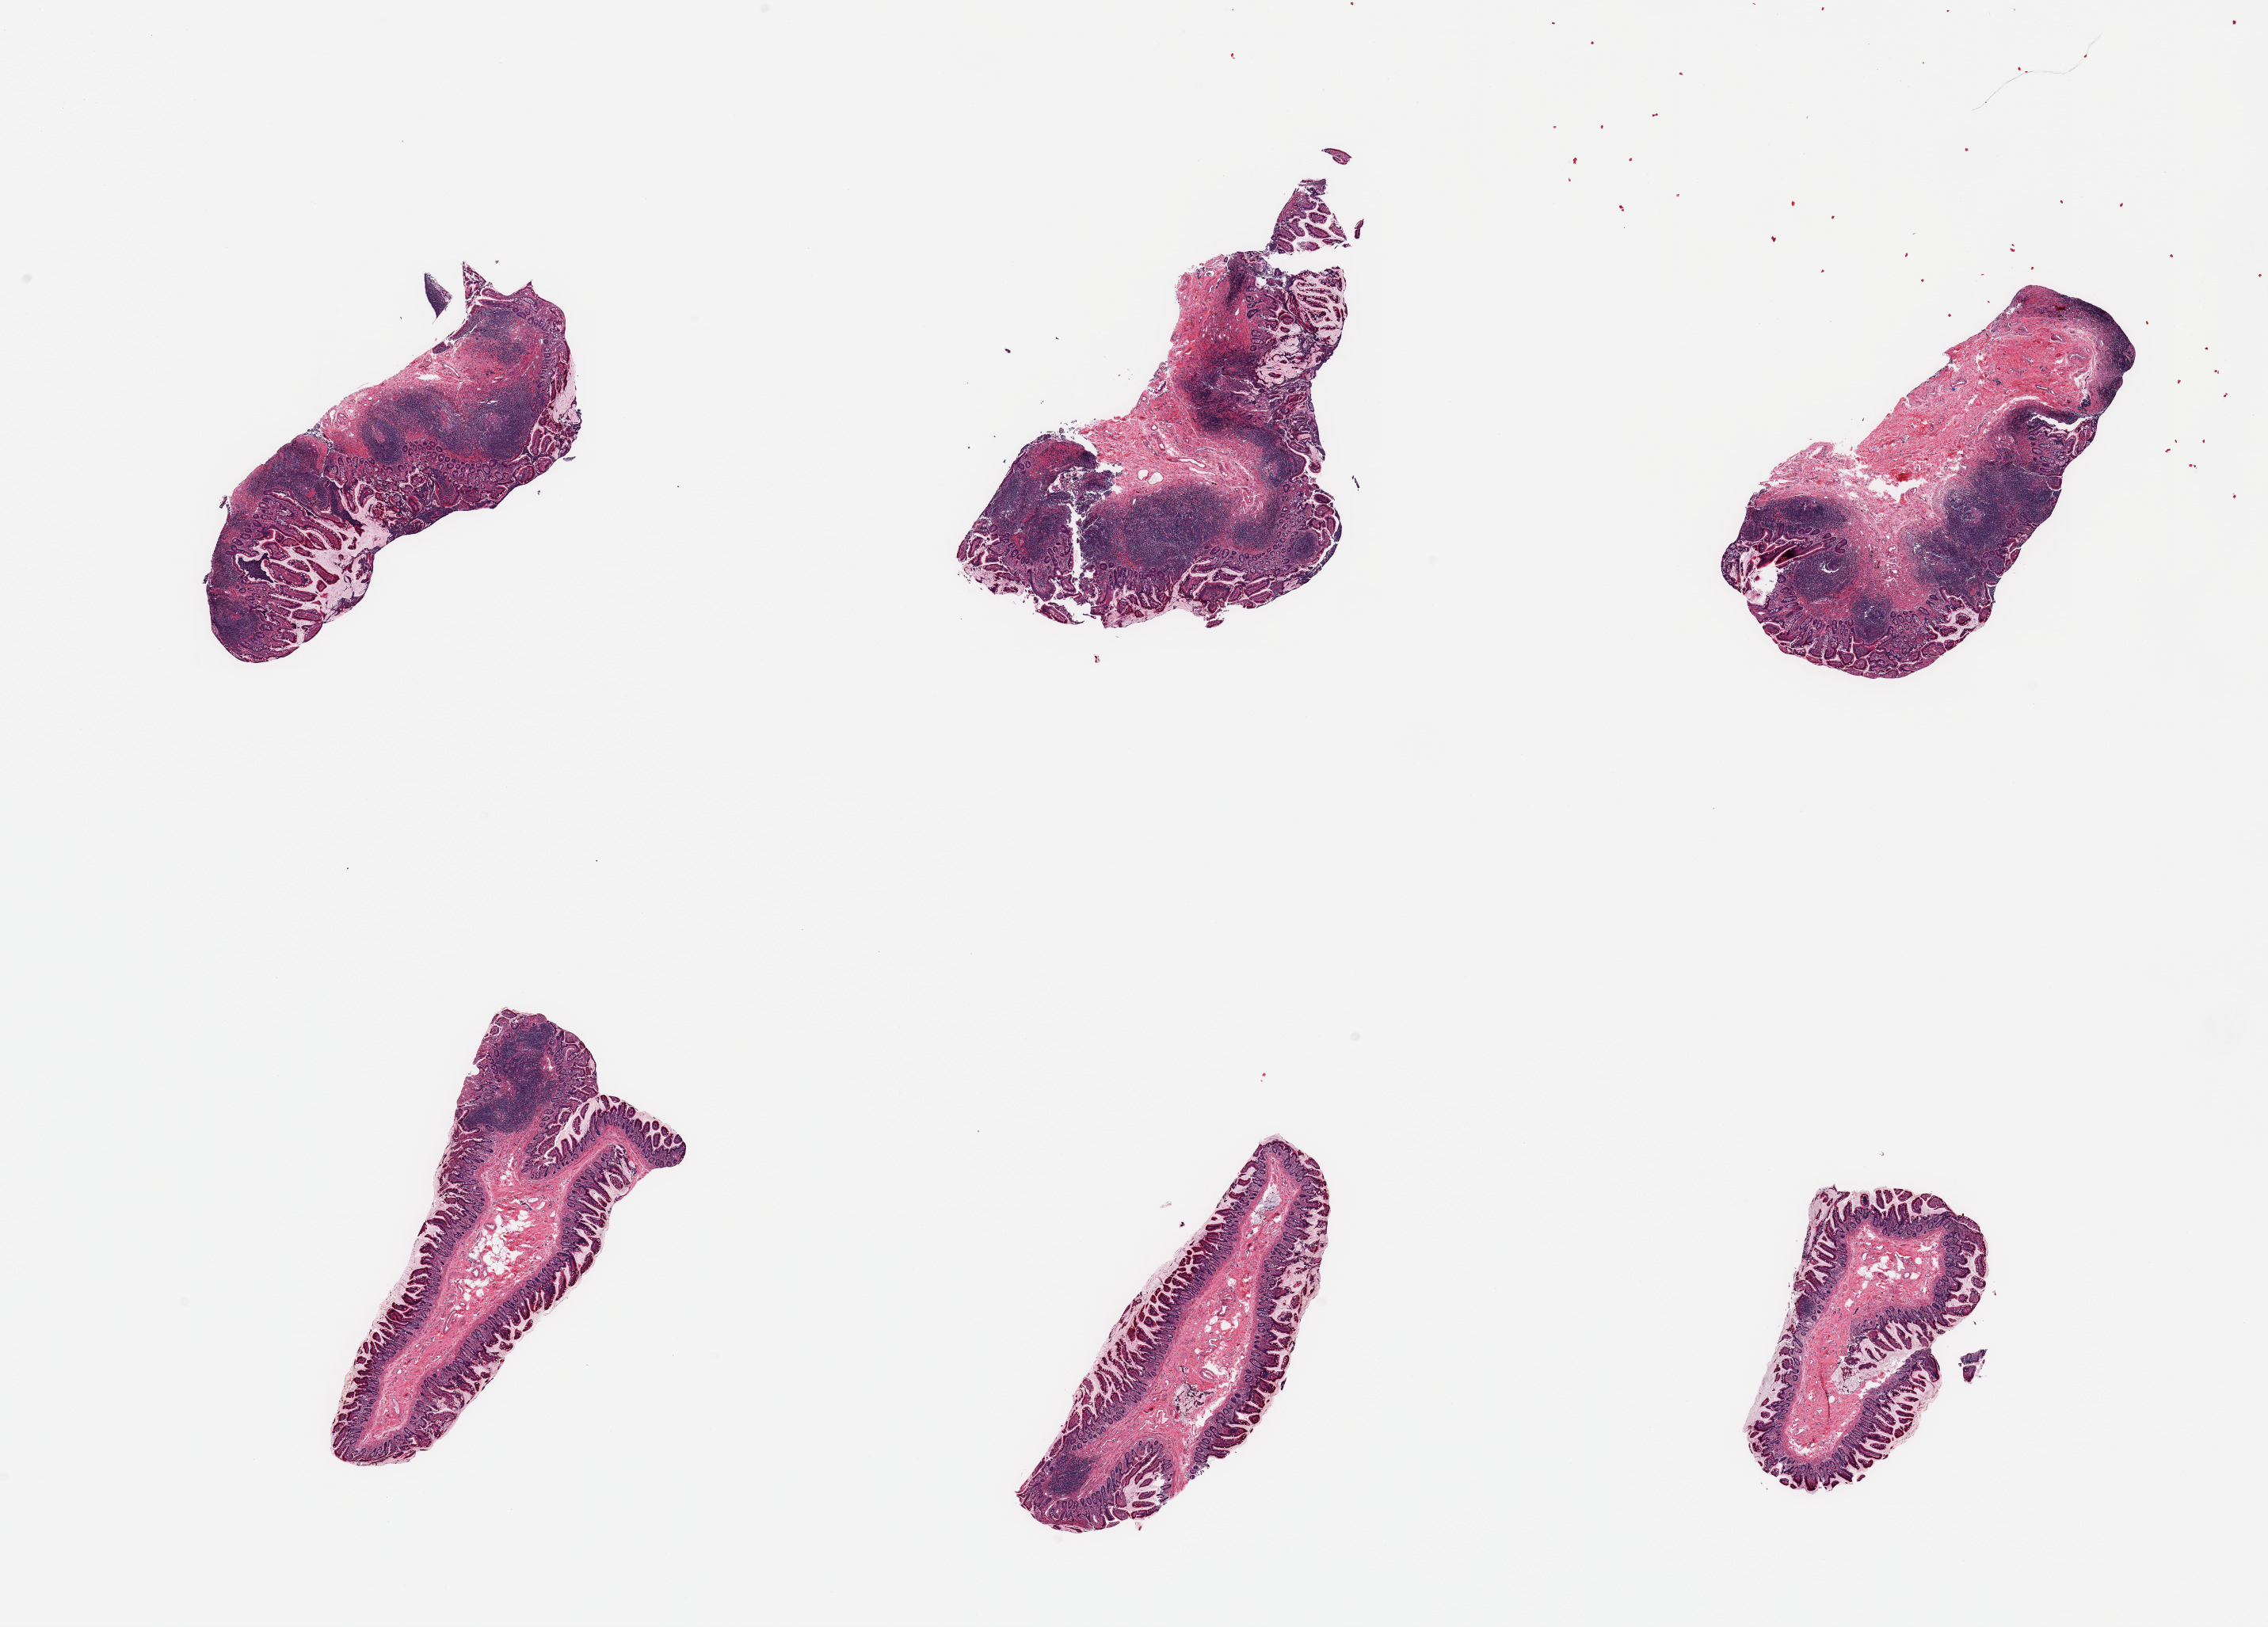
Whole-slide image, haematoxylin and eosin stain, shown as a low-resolution overview of the whole scanned area (about 22.6 x 16.2 mm, from a 20x scan), PAXgene-fixed paraffin-embedded (PFPE) section, section of ileum (target tissue), tissue donor sample. Donor: male.
- review note (as recorded): 6 pieces, well-preserved mucosa, target lymphoid aggregates are ~30% tissue